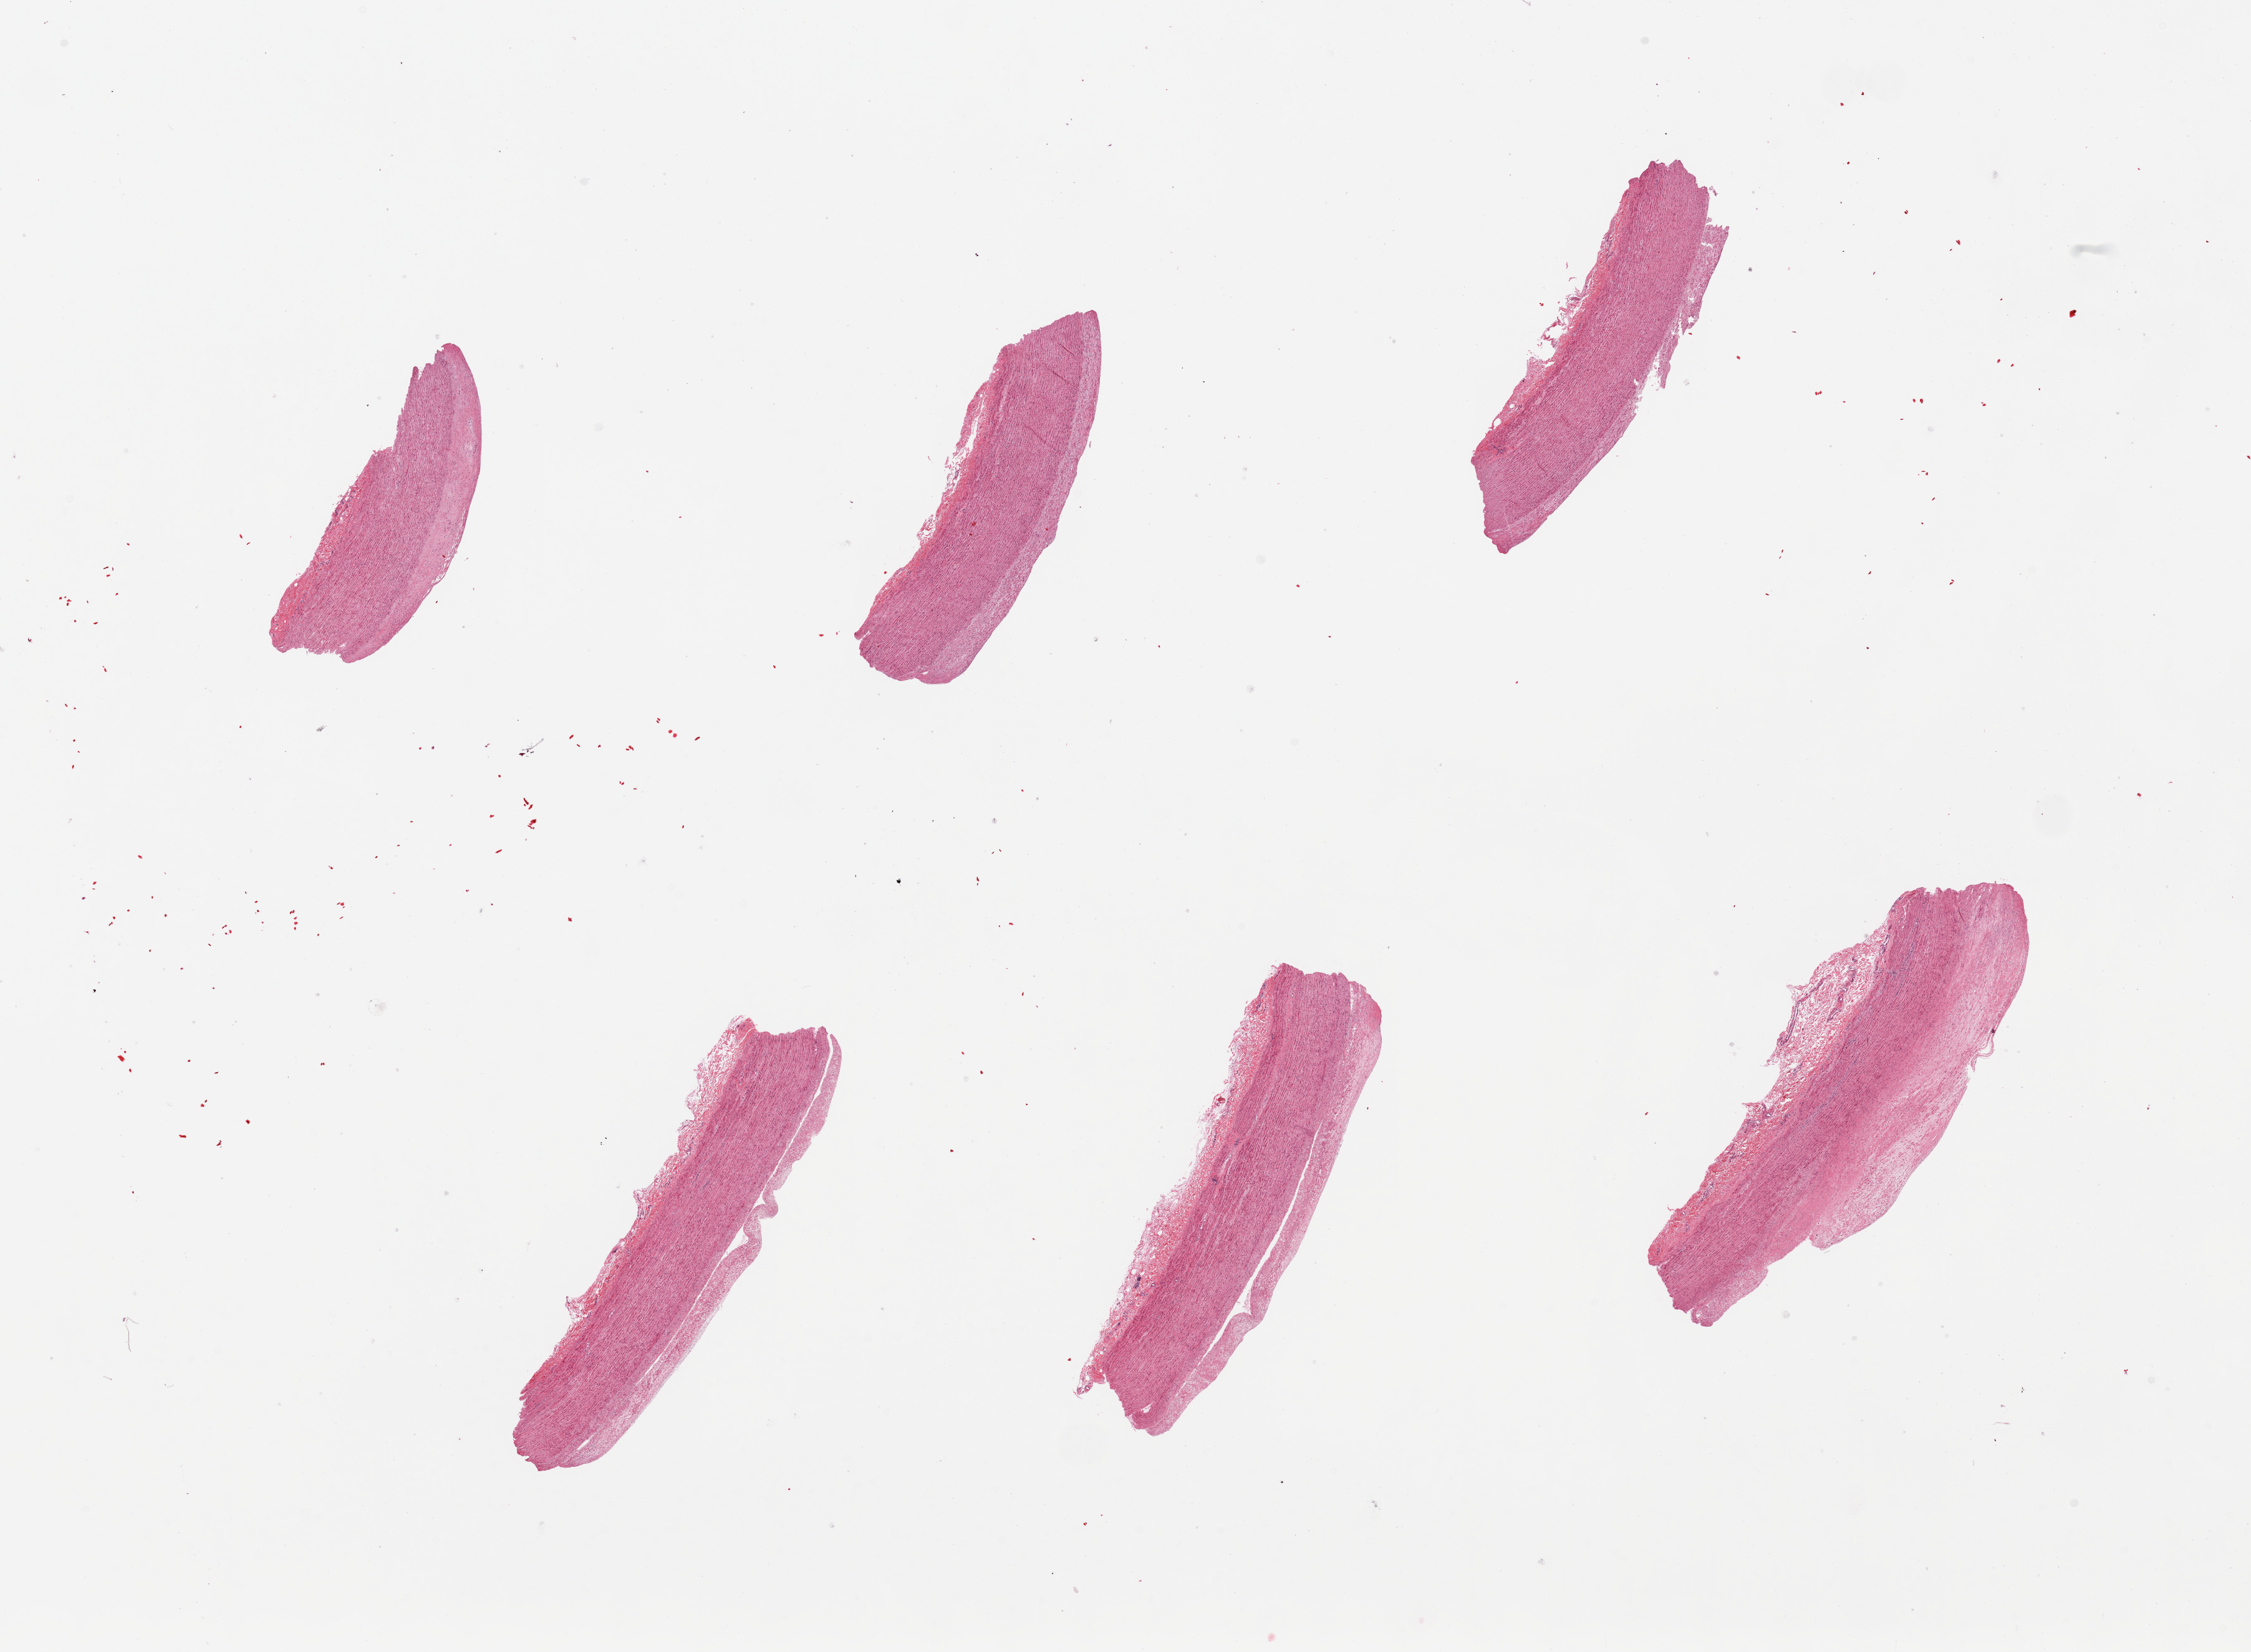
Hematoxylin and eosin (H&E) whole-slide image, brightfield, shown as a low-resolution overview of the whole scanned area (about 28.5 x 21.0 mm), PAXgene-fixed paraffin-embedded (PFPE) section, section of aorta (target tissue), donor tissue sample. Male donor.
Reviewer comment on this tissue sample: 6 pieces, 0.4 to 0.8 mm plaques.